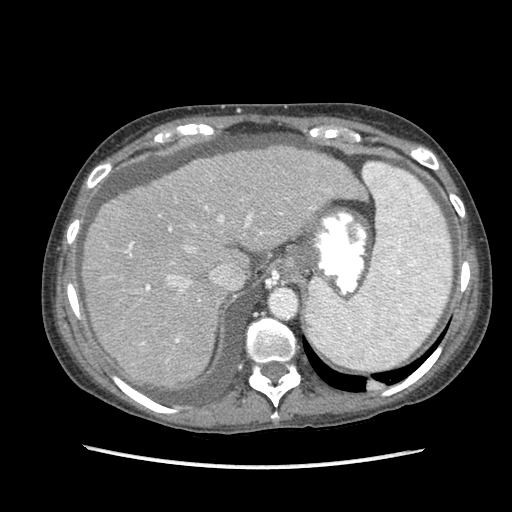
Contrast-enhanced abdominal CT (liver protocol), one axial slice. Slice 68 of 87 in the series (ordered by position). Reconstruction kernel STANDARD. 120 kVp. Soft-tissue window (W 400 / L 40 HU). 512 × 512 image matrix, field of view 340 × 340 mm. From the clinical record (not read from this slice): diagnosis: hepatocellular carcinoma (patient treated with transarterial chemoembolisation; whether this scan precedes or follows treatment is not stated here); TNM stage (as recorded): Stage-IIIB; Child-Pugh class: A; tumour differentiation: no biopsy.
Structures marked on this image (semi-automatically segmented with operator editing):
- liver parenchyma outside the tumour (the mass and vessels are separate outlines, so this box may not span the whole liver): box from (x=82, y=146) to (x=362, y=386) px
- liver vessels: (x=125, y=199)–(x=314, y=345)